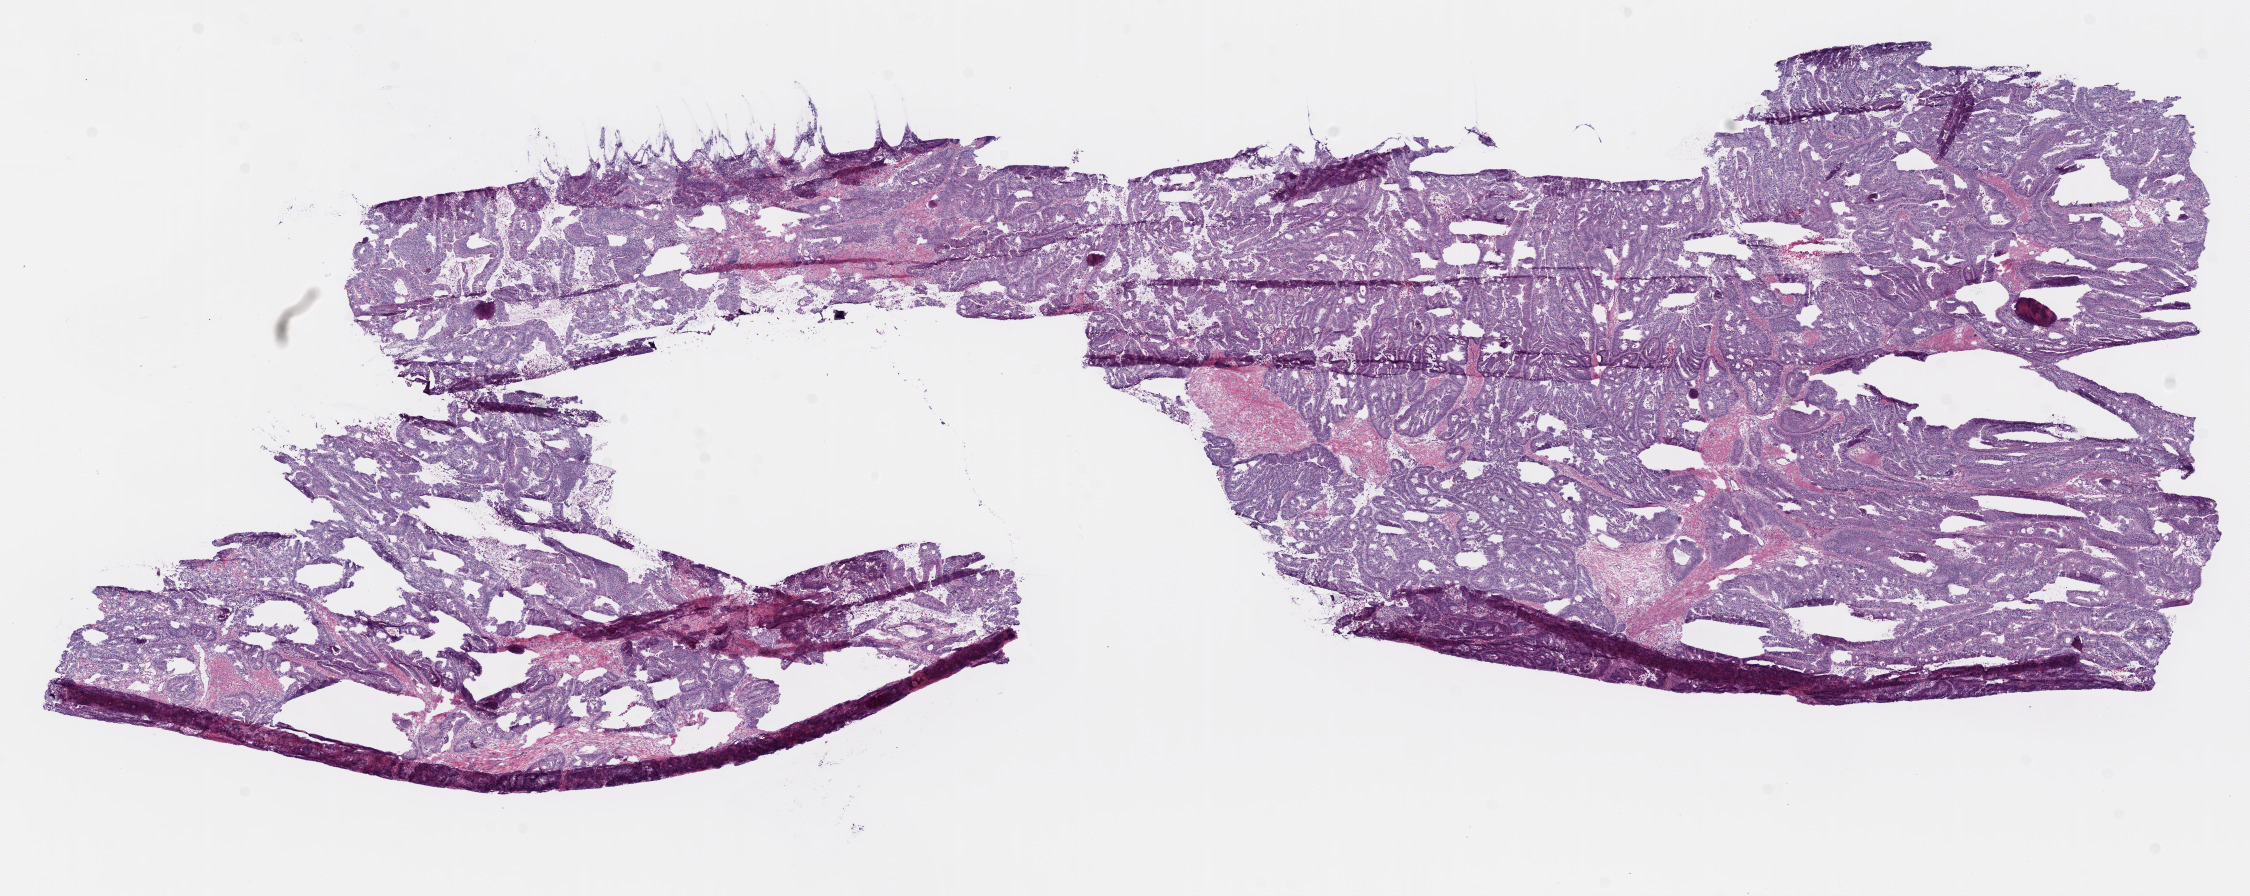
H&E-stained whole-slide image, whole scanned area (about 18.1 x 7.2 mm) shown as a low-resolution overview, frozen section from the bottom of the tissue portion, sample: primary tumour, colon. Female, age 57 years at initial diagnosis. Slide review estimates, as recorded: tumour cells 90%, tumour nuclei 90%, normal cells 0%, stromal cells 5%, necrosis 5%.
* lymph nodes positive (case pathology): 0 of 25 examined
* pathologic diagnosis: Adenocarcinoma, NOS (ascending colon)
* AJCC pathologic stage: IV (6th edition)